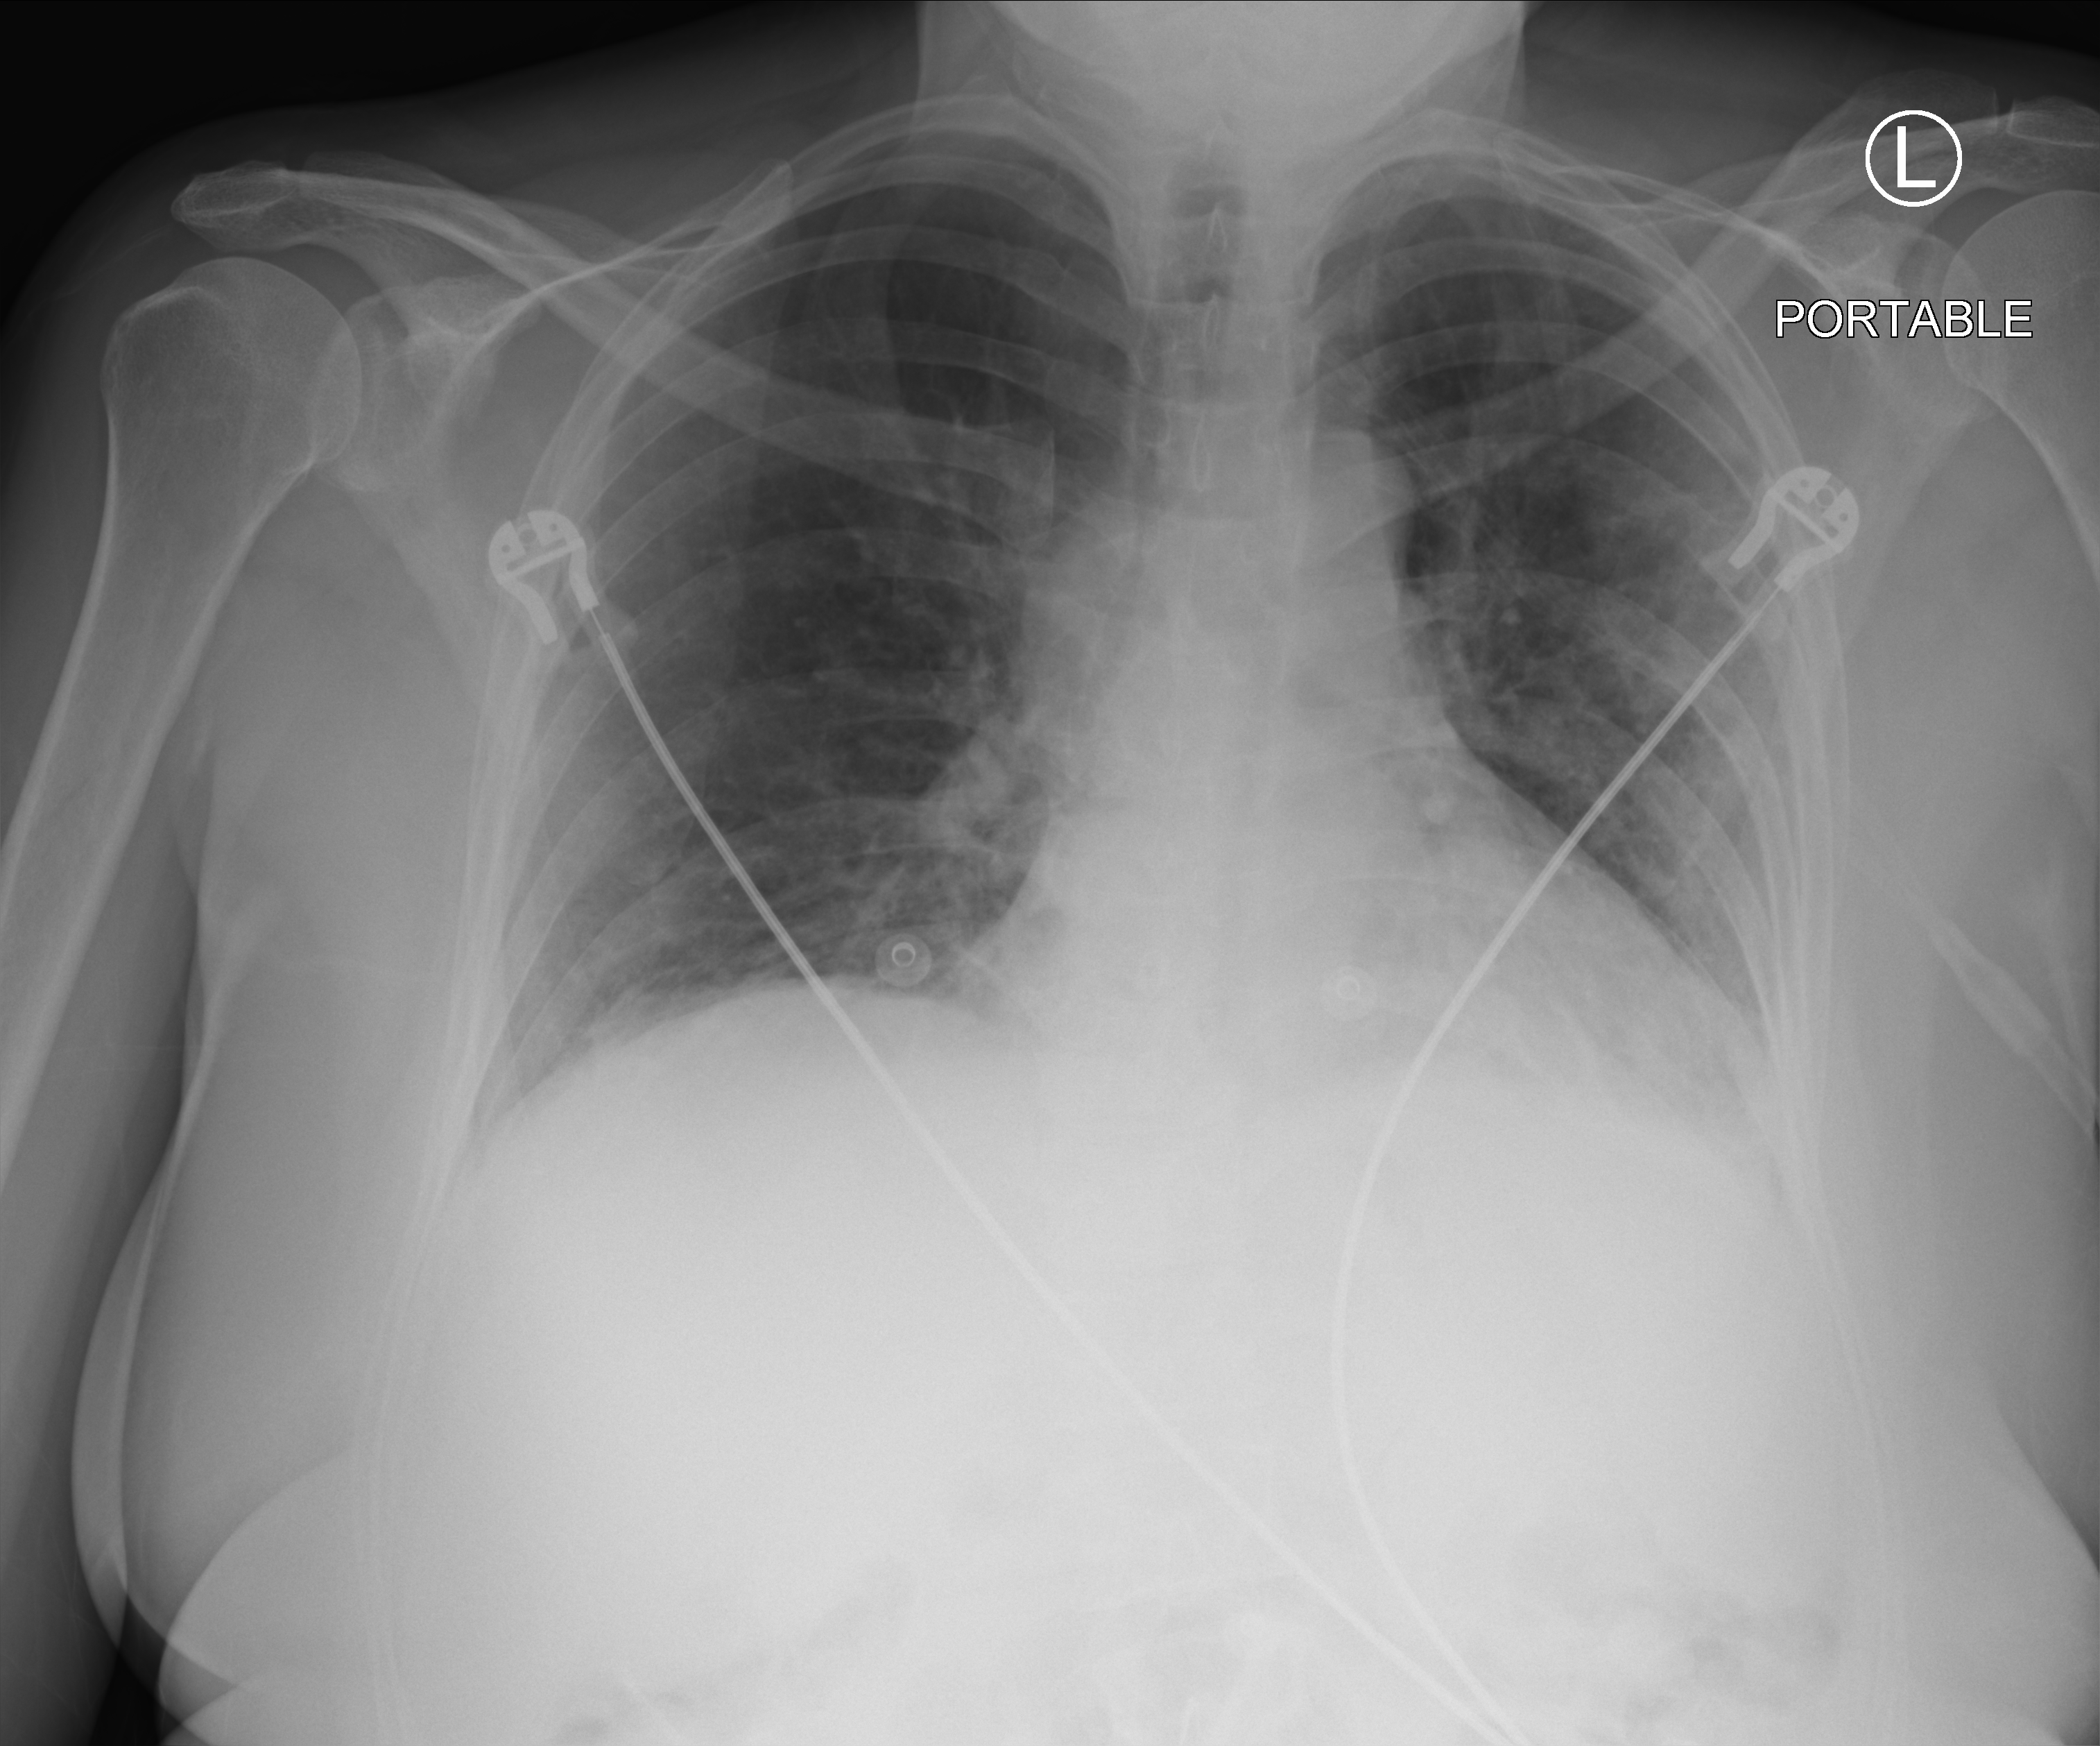
Chest X-ray (portable); anteroposterior (AP) projection. Patient hospitalised with COVID-19; female, aged 18–59 years.
Hospital-stay facts (about this admission, not read from this image; timing relative to this image not recorded):
- smoking status (admission record): never